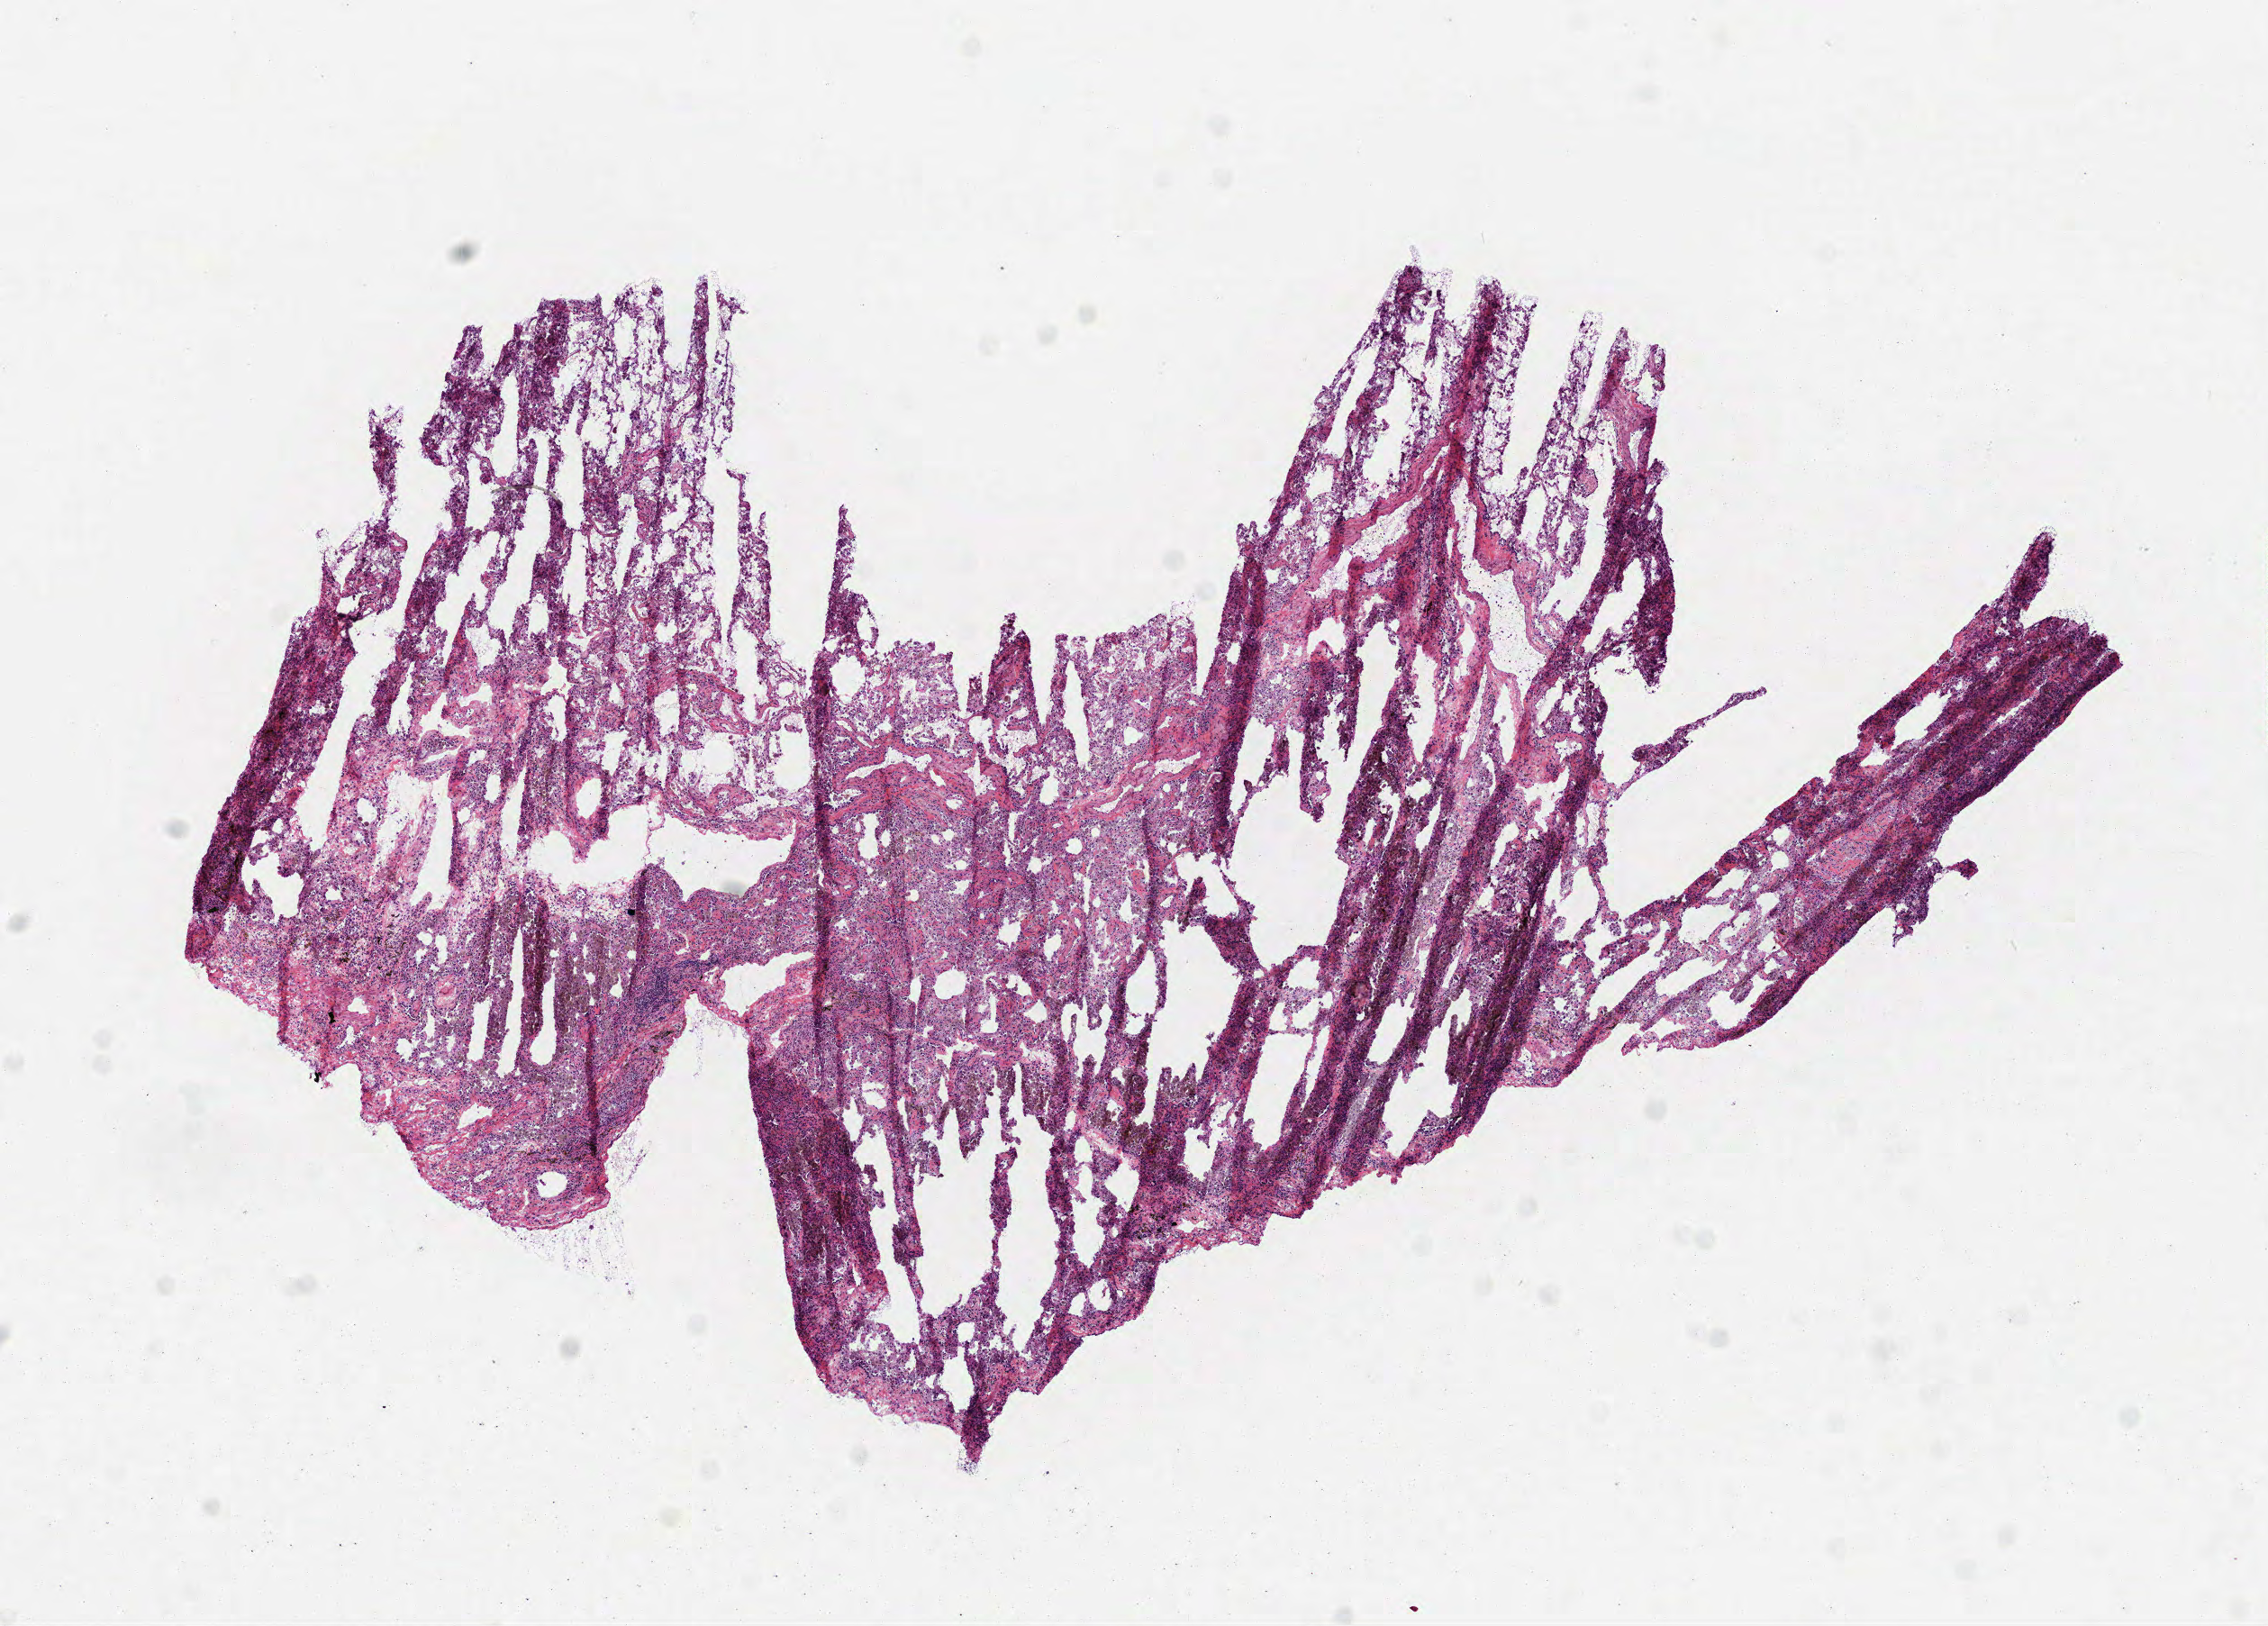
Hematoxylin and eosin (H&E) stained whole-slide image, shown as a low-resolution overview of the whole scanned area (about 10.2 x 7.3 mm, acquisition: 40x scan), frozen section from the top of the tissue portion, lung, solid tissue normal (non-tumour tissue) sample. Female patient; age at initial diagnosis 54 years. Infiltration values recorded for this section: lymphocyte infiltration 5%, monocyte infiltration 30%, neutrophil infiltration 0%.
• this section: solid tissue normal sample (biorepository sample class)
• patient diagnosis: Adenocarcinoma, NOS (upper lobe, lung)